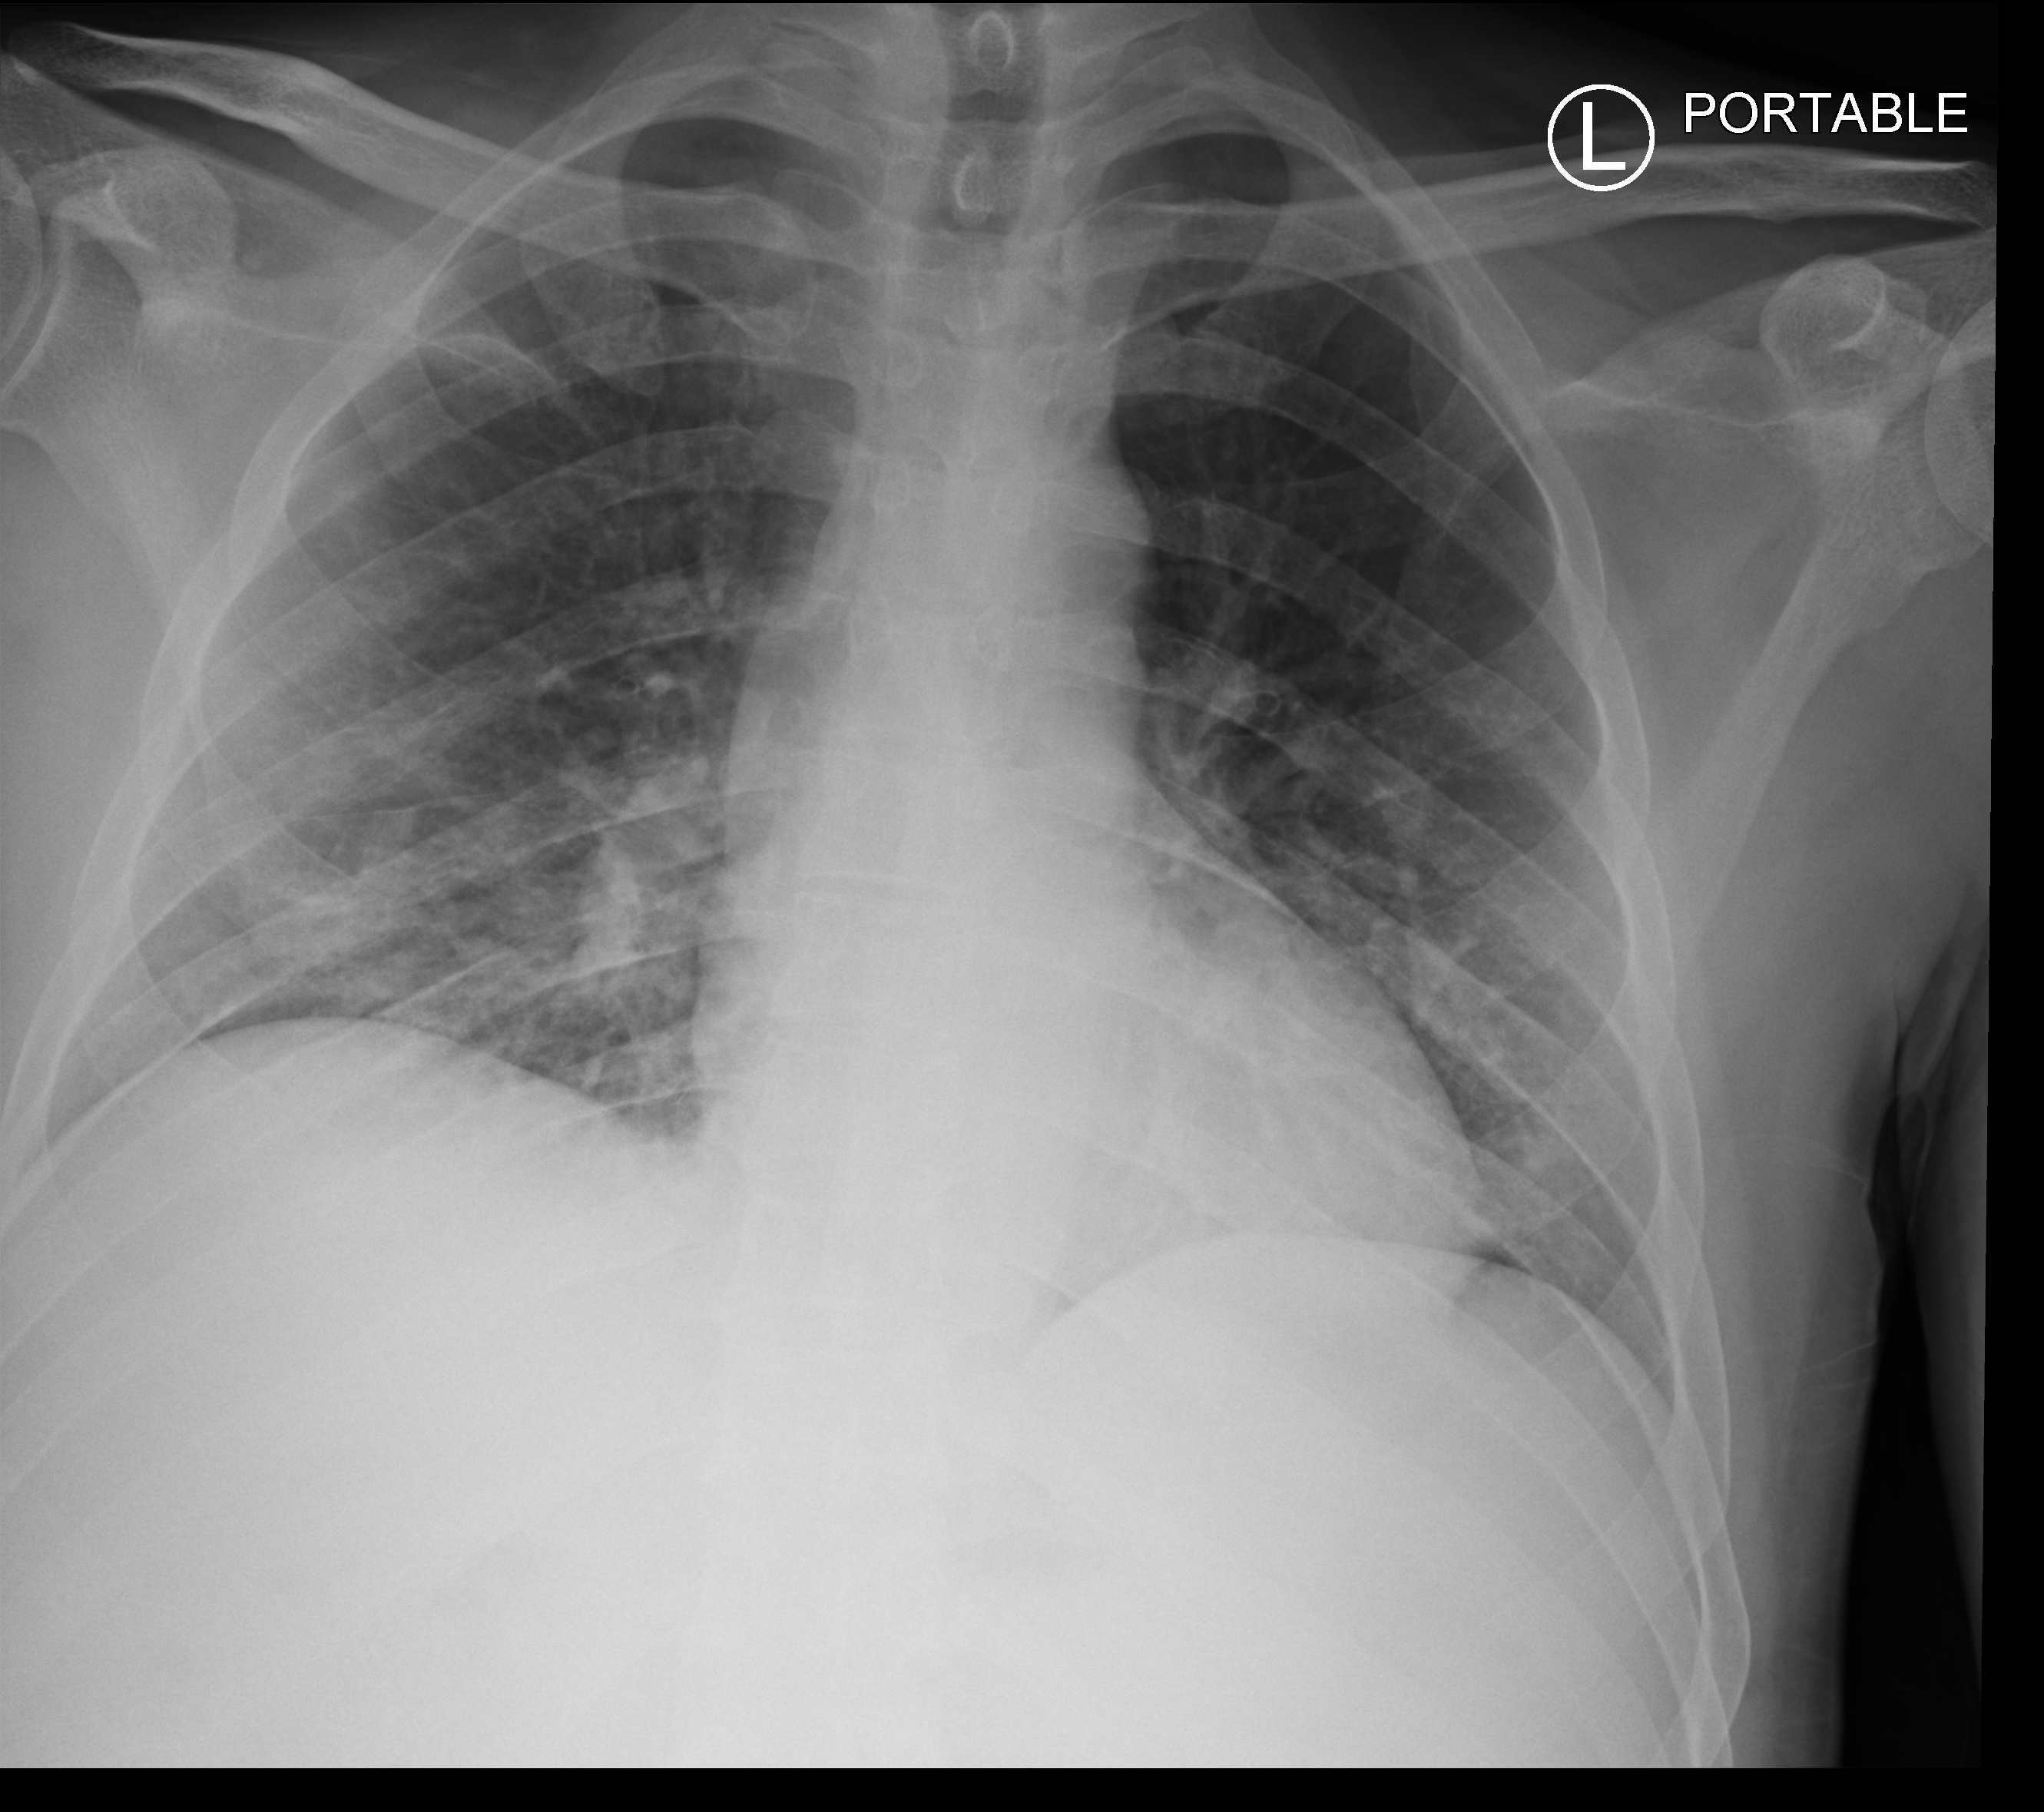
Bedside chest radiograph (computed radiography), anteroposterior (AP) projection. Patient hospitalised with COVID-19; male, aged 18–59 years.
From the hospital-stay record, not from the radiograph (when in the stay this image was taken is not recorded): other chronic lung disease (admission record): no.